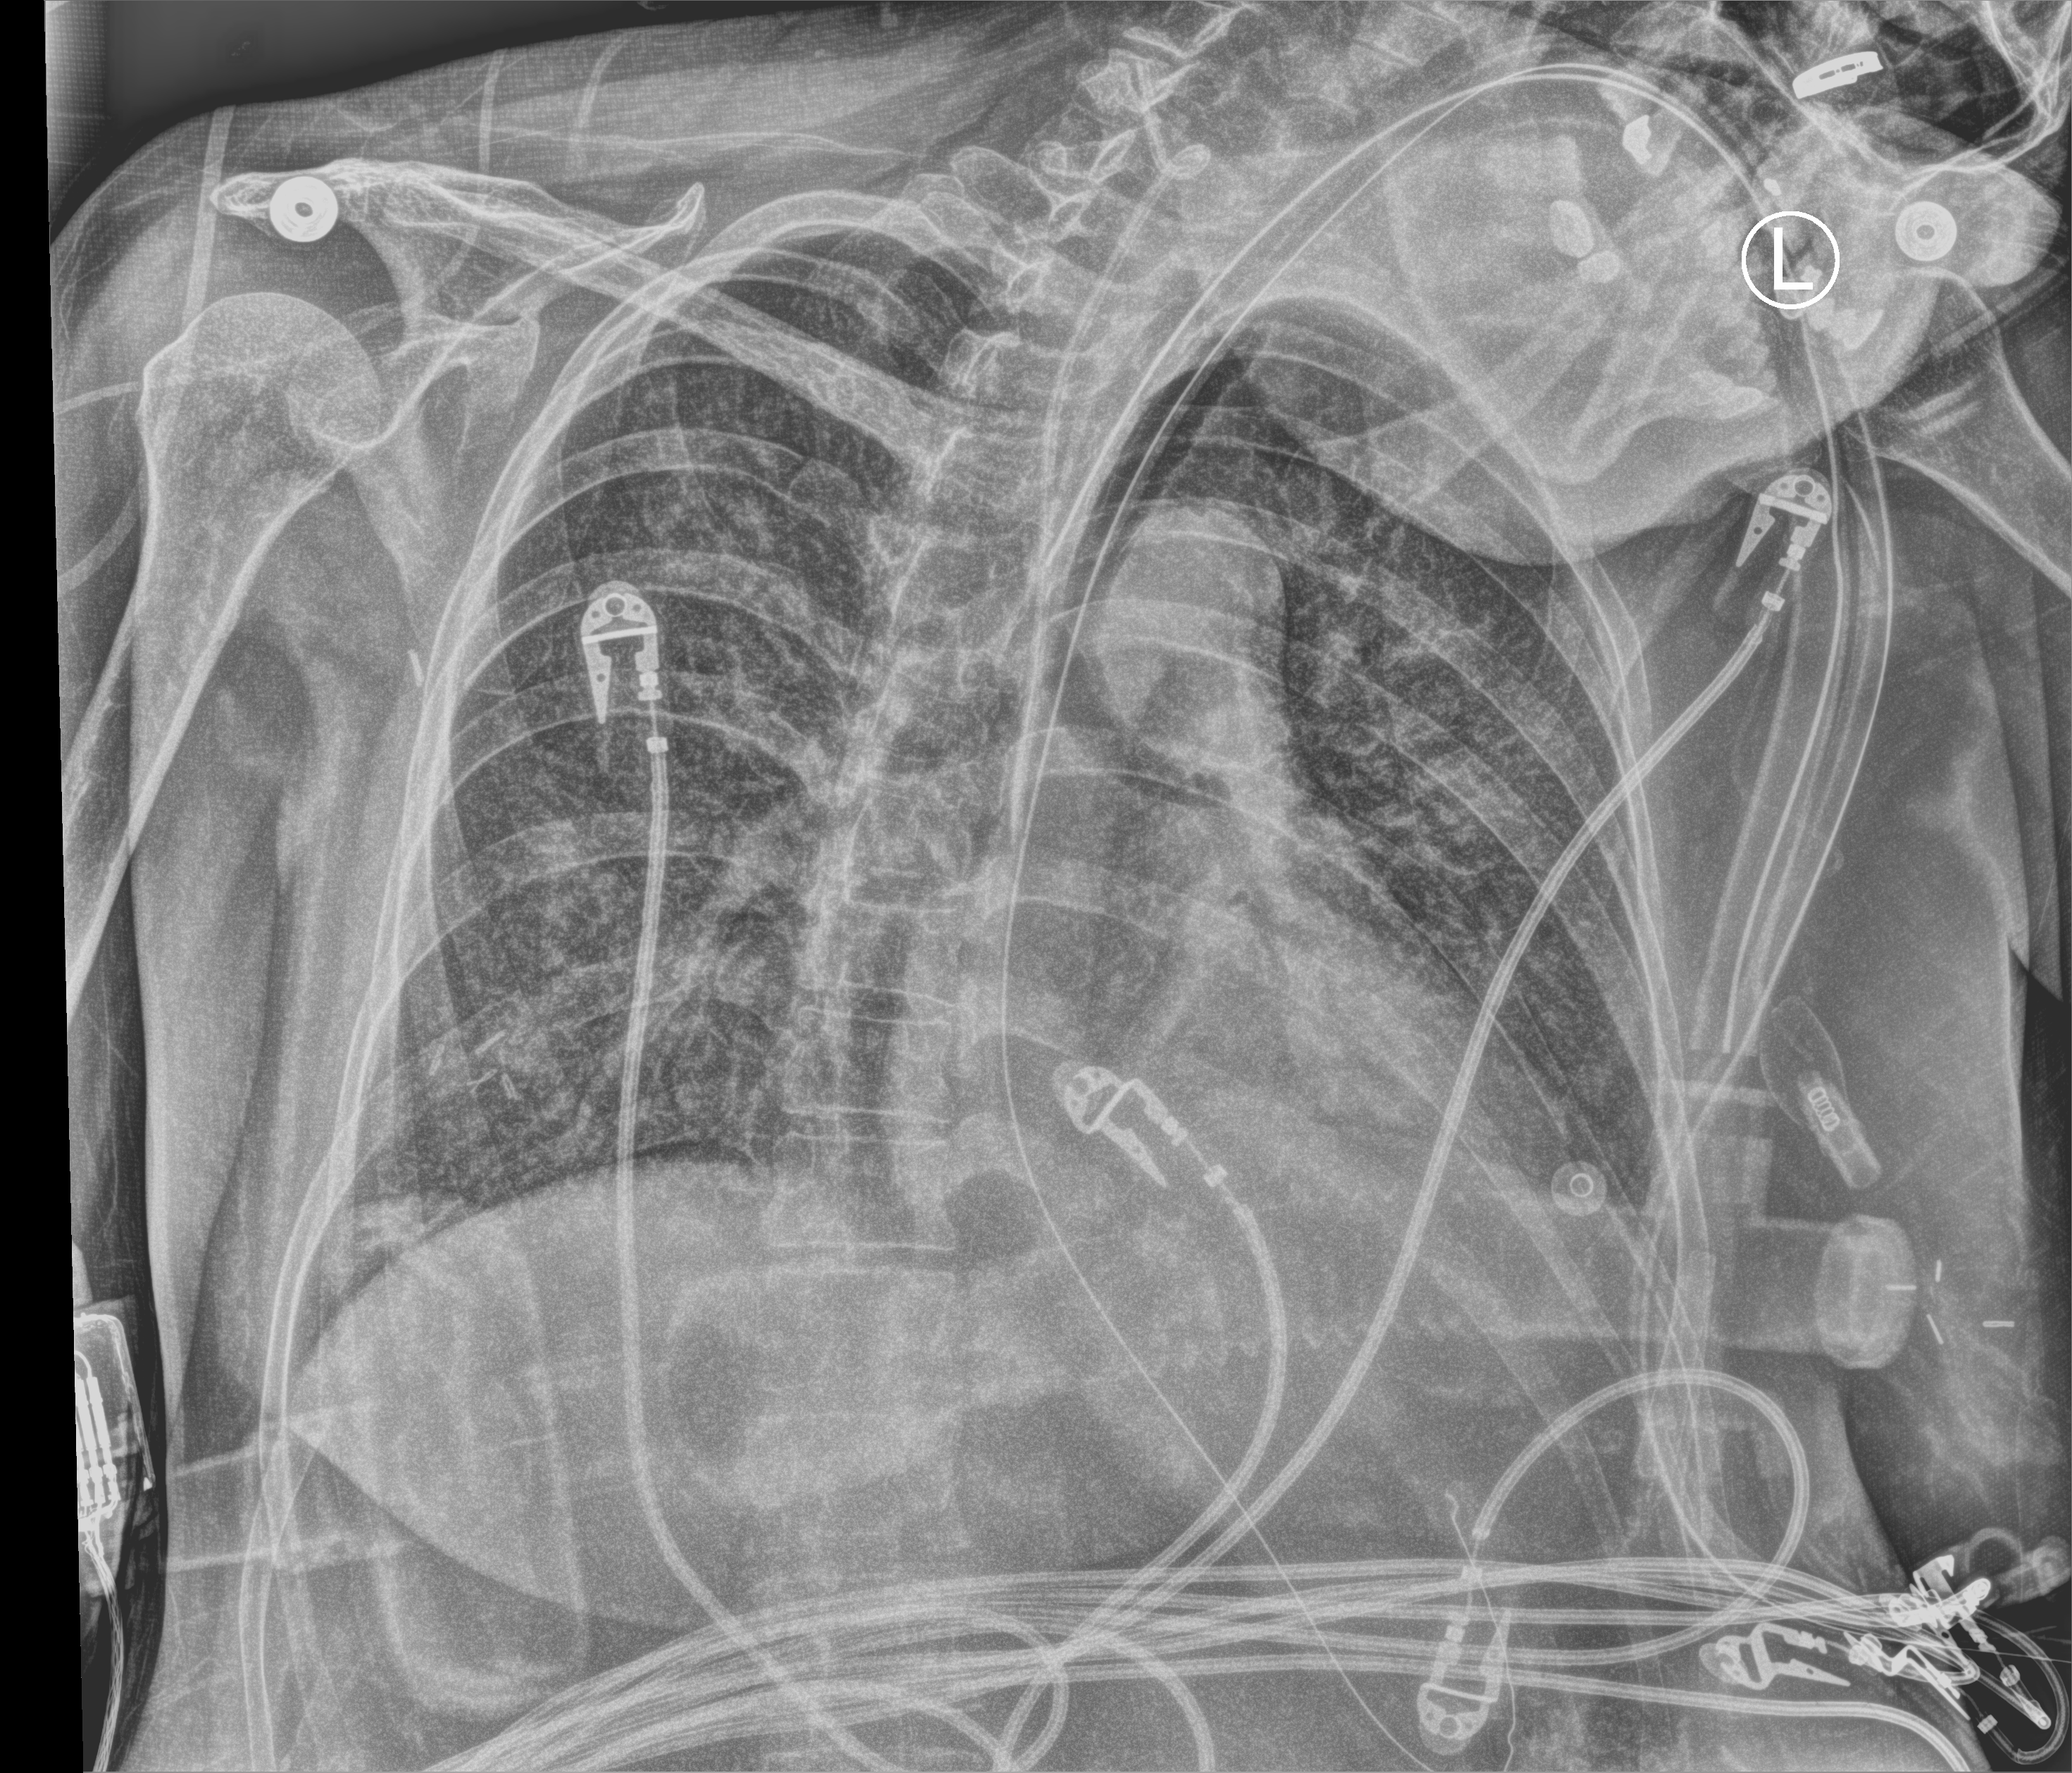
Bedside chest radiograph (computed radiography), anteroposterior (AP) projection. Patient hospitalised with COVID-19; female, aged 18–59 years.
Hospital-stay facts (about this admission, not read from this image; timing relative to this image not recorded):
- chronic kidney disease (admission record): no